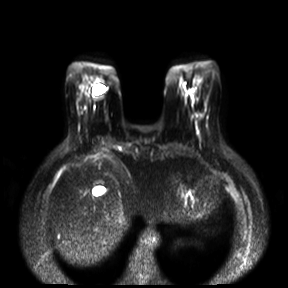
Breast MRI, one axial slice. Diffusion-weighted series; image 2 of 4 stored at this slice position (different b-values; order by instance number). 3 T. 4 mm slice thickness. 288 × 288 image matrix, field of view 360 × 360 mm. Female patient.
Structures marked on this image (outlined manually by an expert reader):
- tumour on diffusion-weighted imaging: bounding box (x1, y1, x2, y2) in pixels: (186, 90, 194, 98)